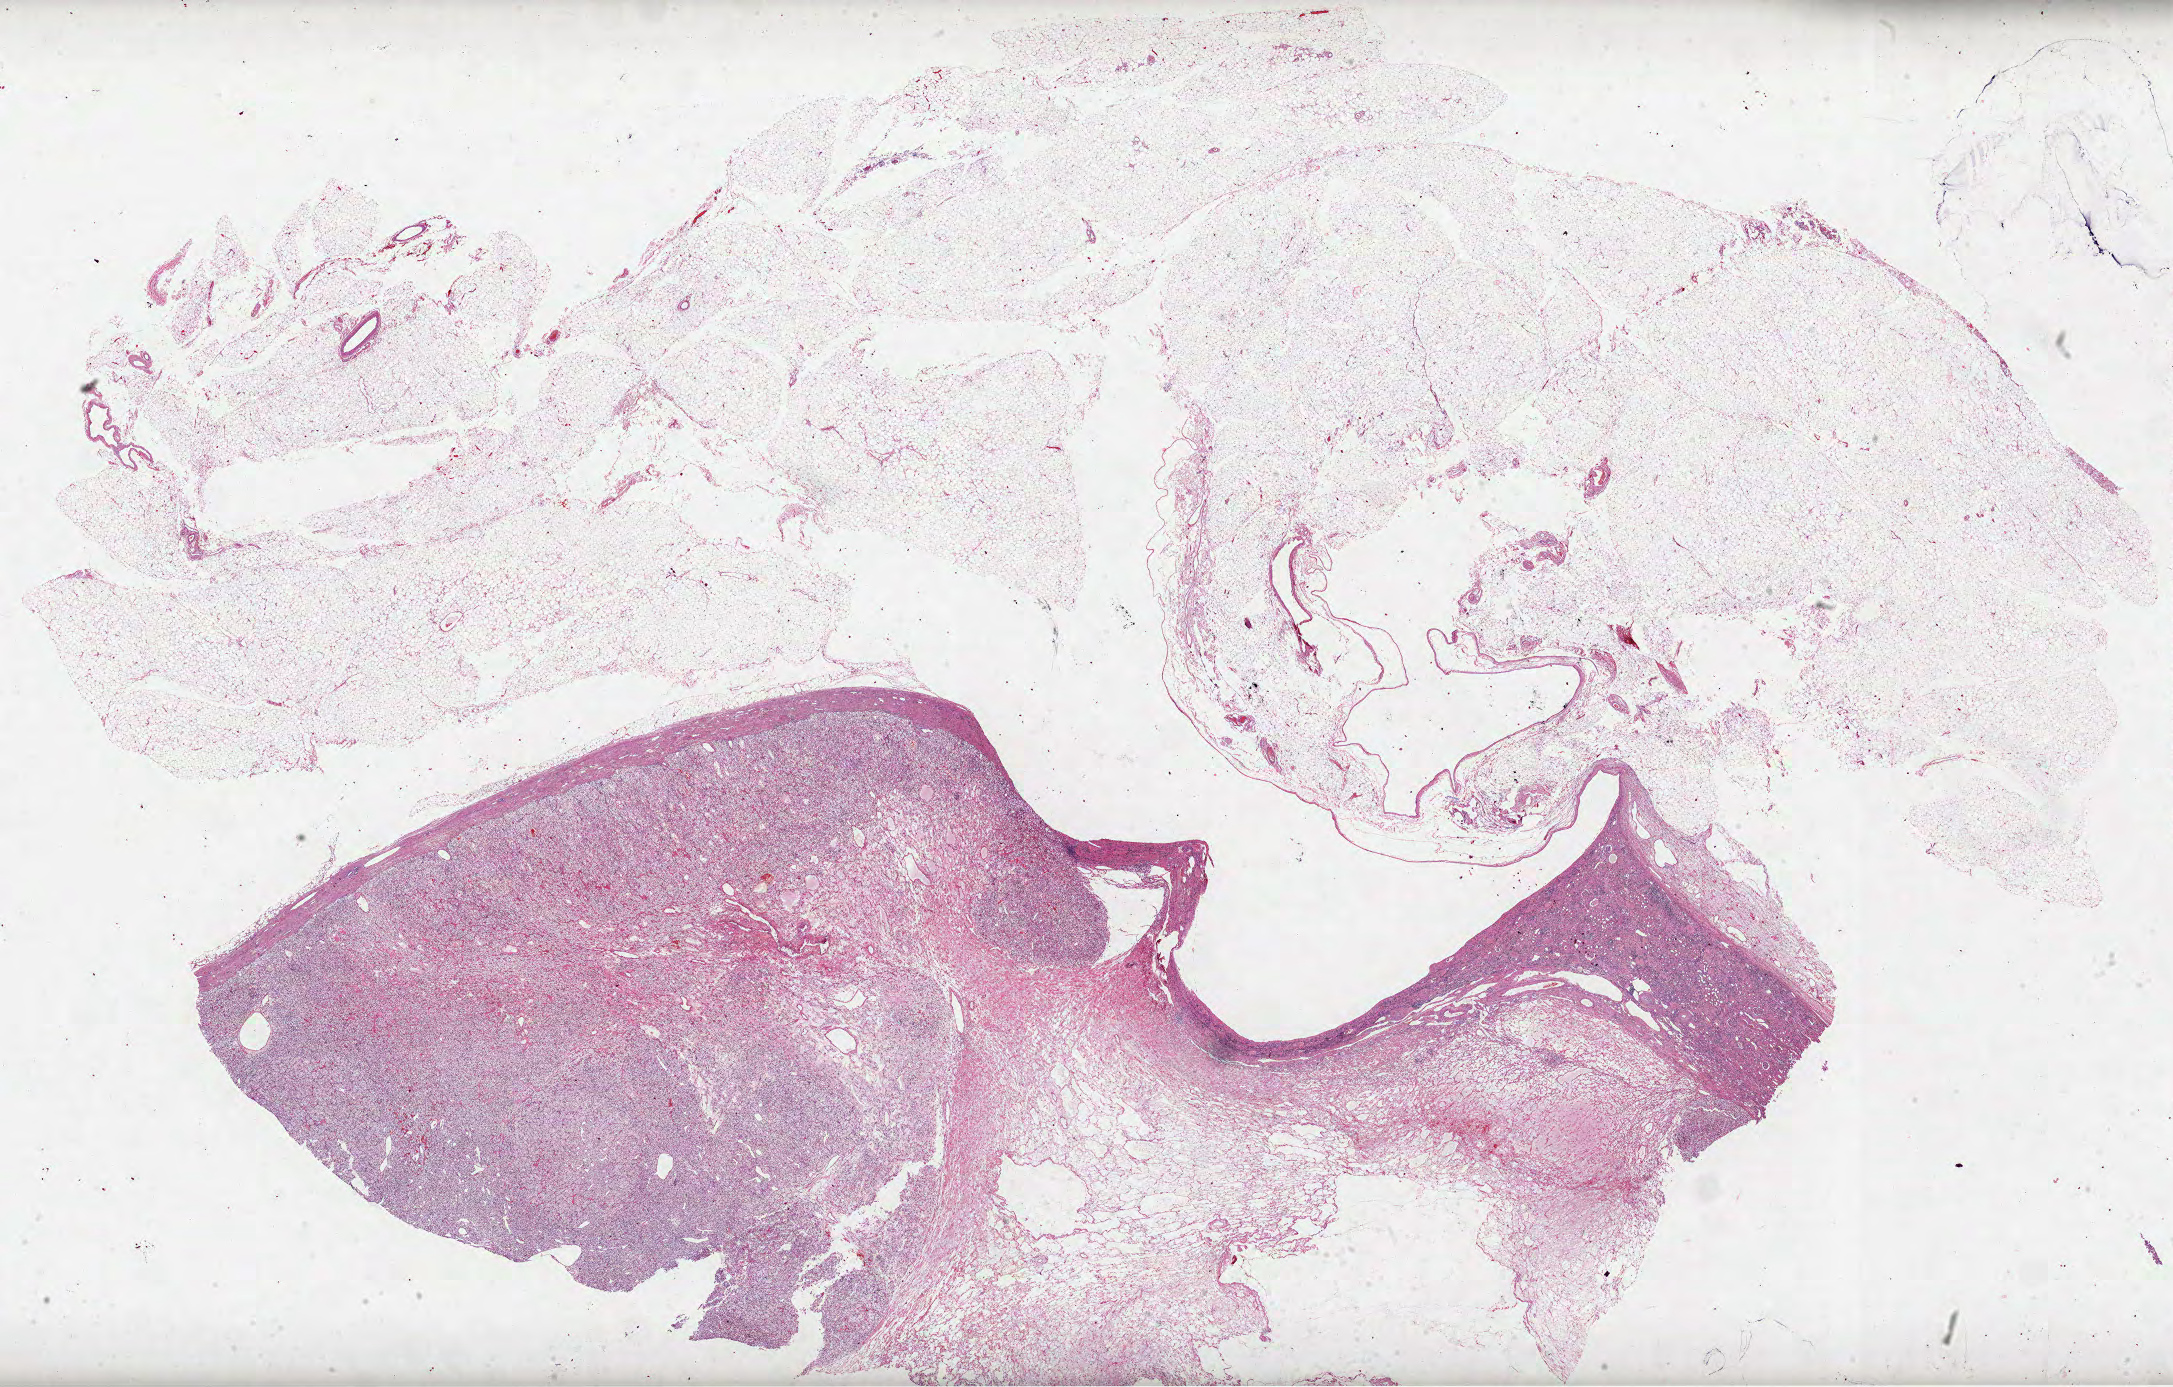
H&E-stained whole-slide image, a low-resolution overview of the entire scanned area, about 35.1 x 22.4 mm (acquisition: 40x scan), formalin-fixed paraffin-embedded (FFPE) diagnostic section, primary tumour sample from the kidney. Patient: female, age at initial diagnosis 49 years. Histologic grade: G3 (poorly differentiated).
Pathologic diagnosis: Clear cell adenocarcinoma, NOS. AJCC pathologic stage: I.